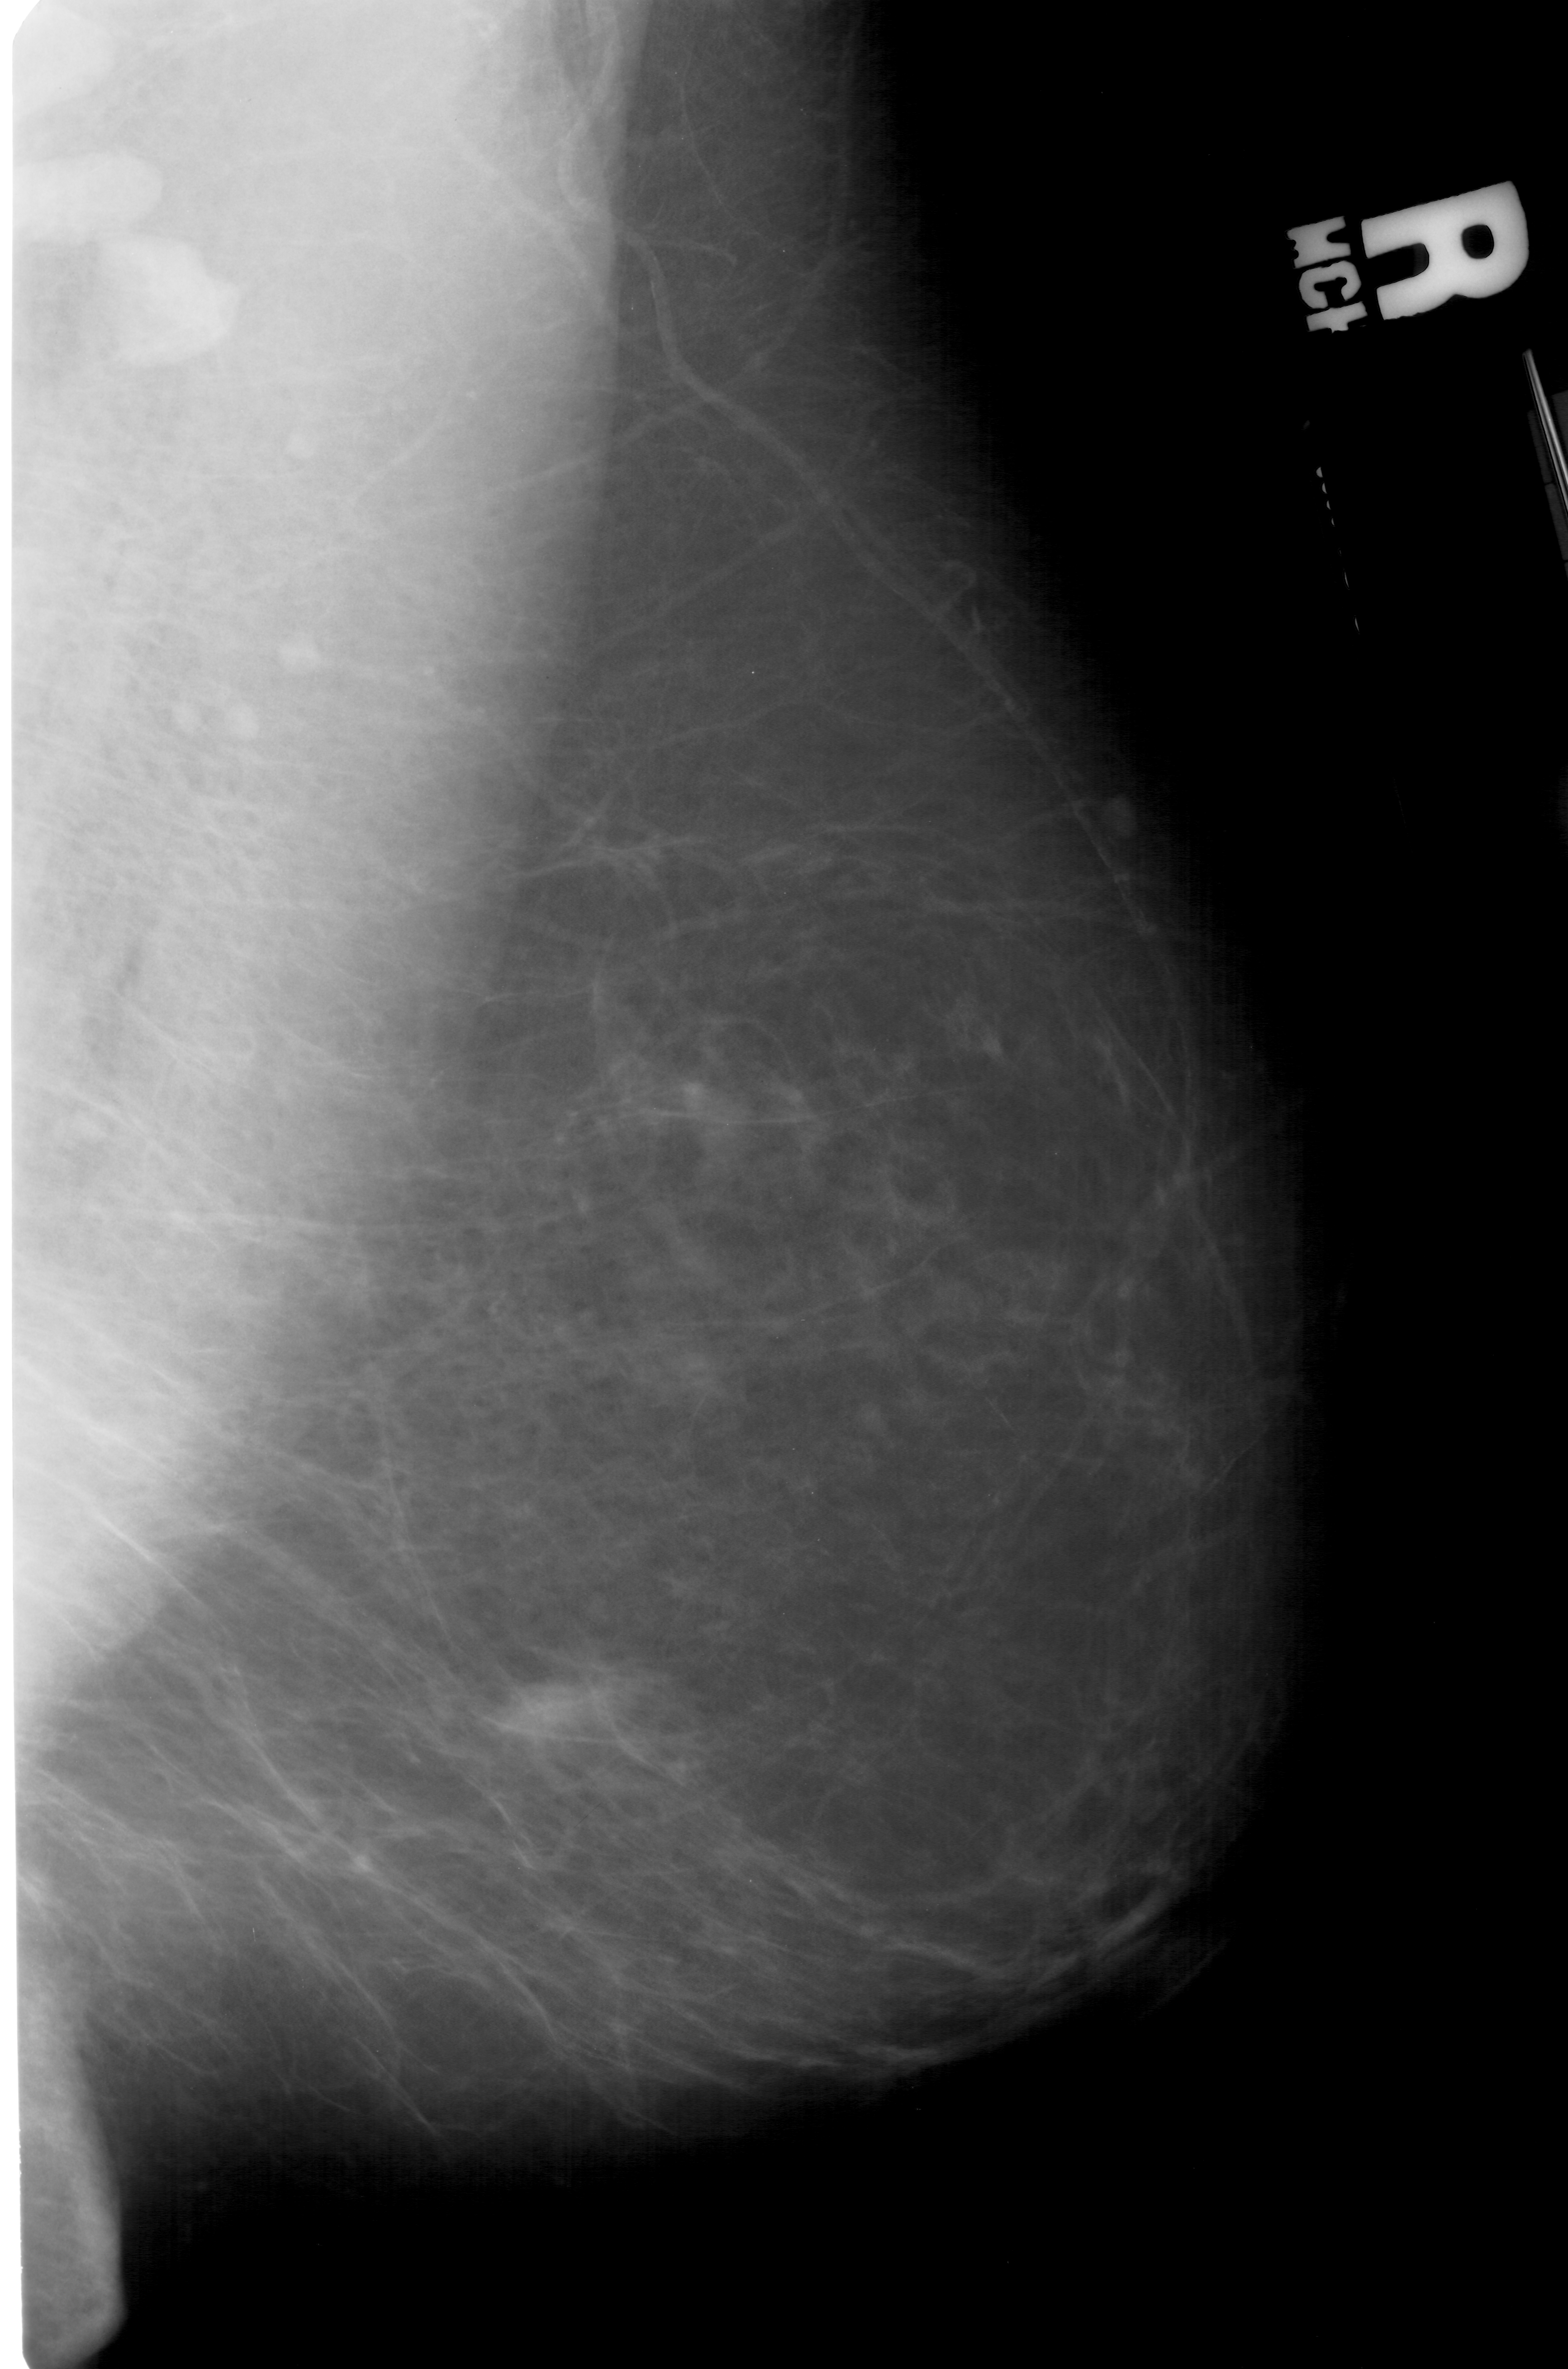
Scanned film-screen mammogram; right breast; MLO view; BI-RADS breast density category 2 (scale 1–4); 1568 × 2369 image matrix.
Expert-marked regions of interest on this image (one box per marked abnormality):
- mass, shape focal asymmetric density, margins ill defined; BI-RADS assessment category 4; pathology (as recorded): malignant: box from (x=477, y=1671) to (x=603, y=1750) px